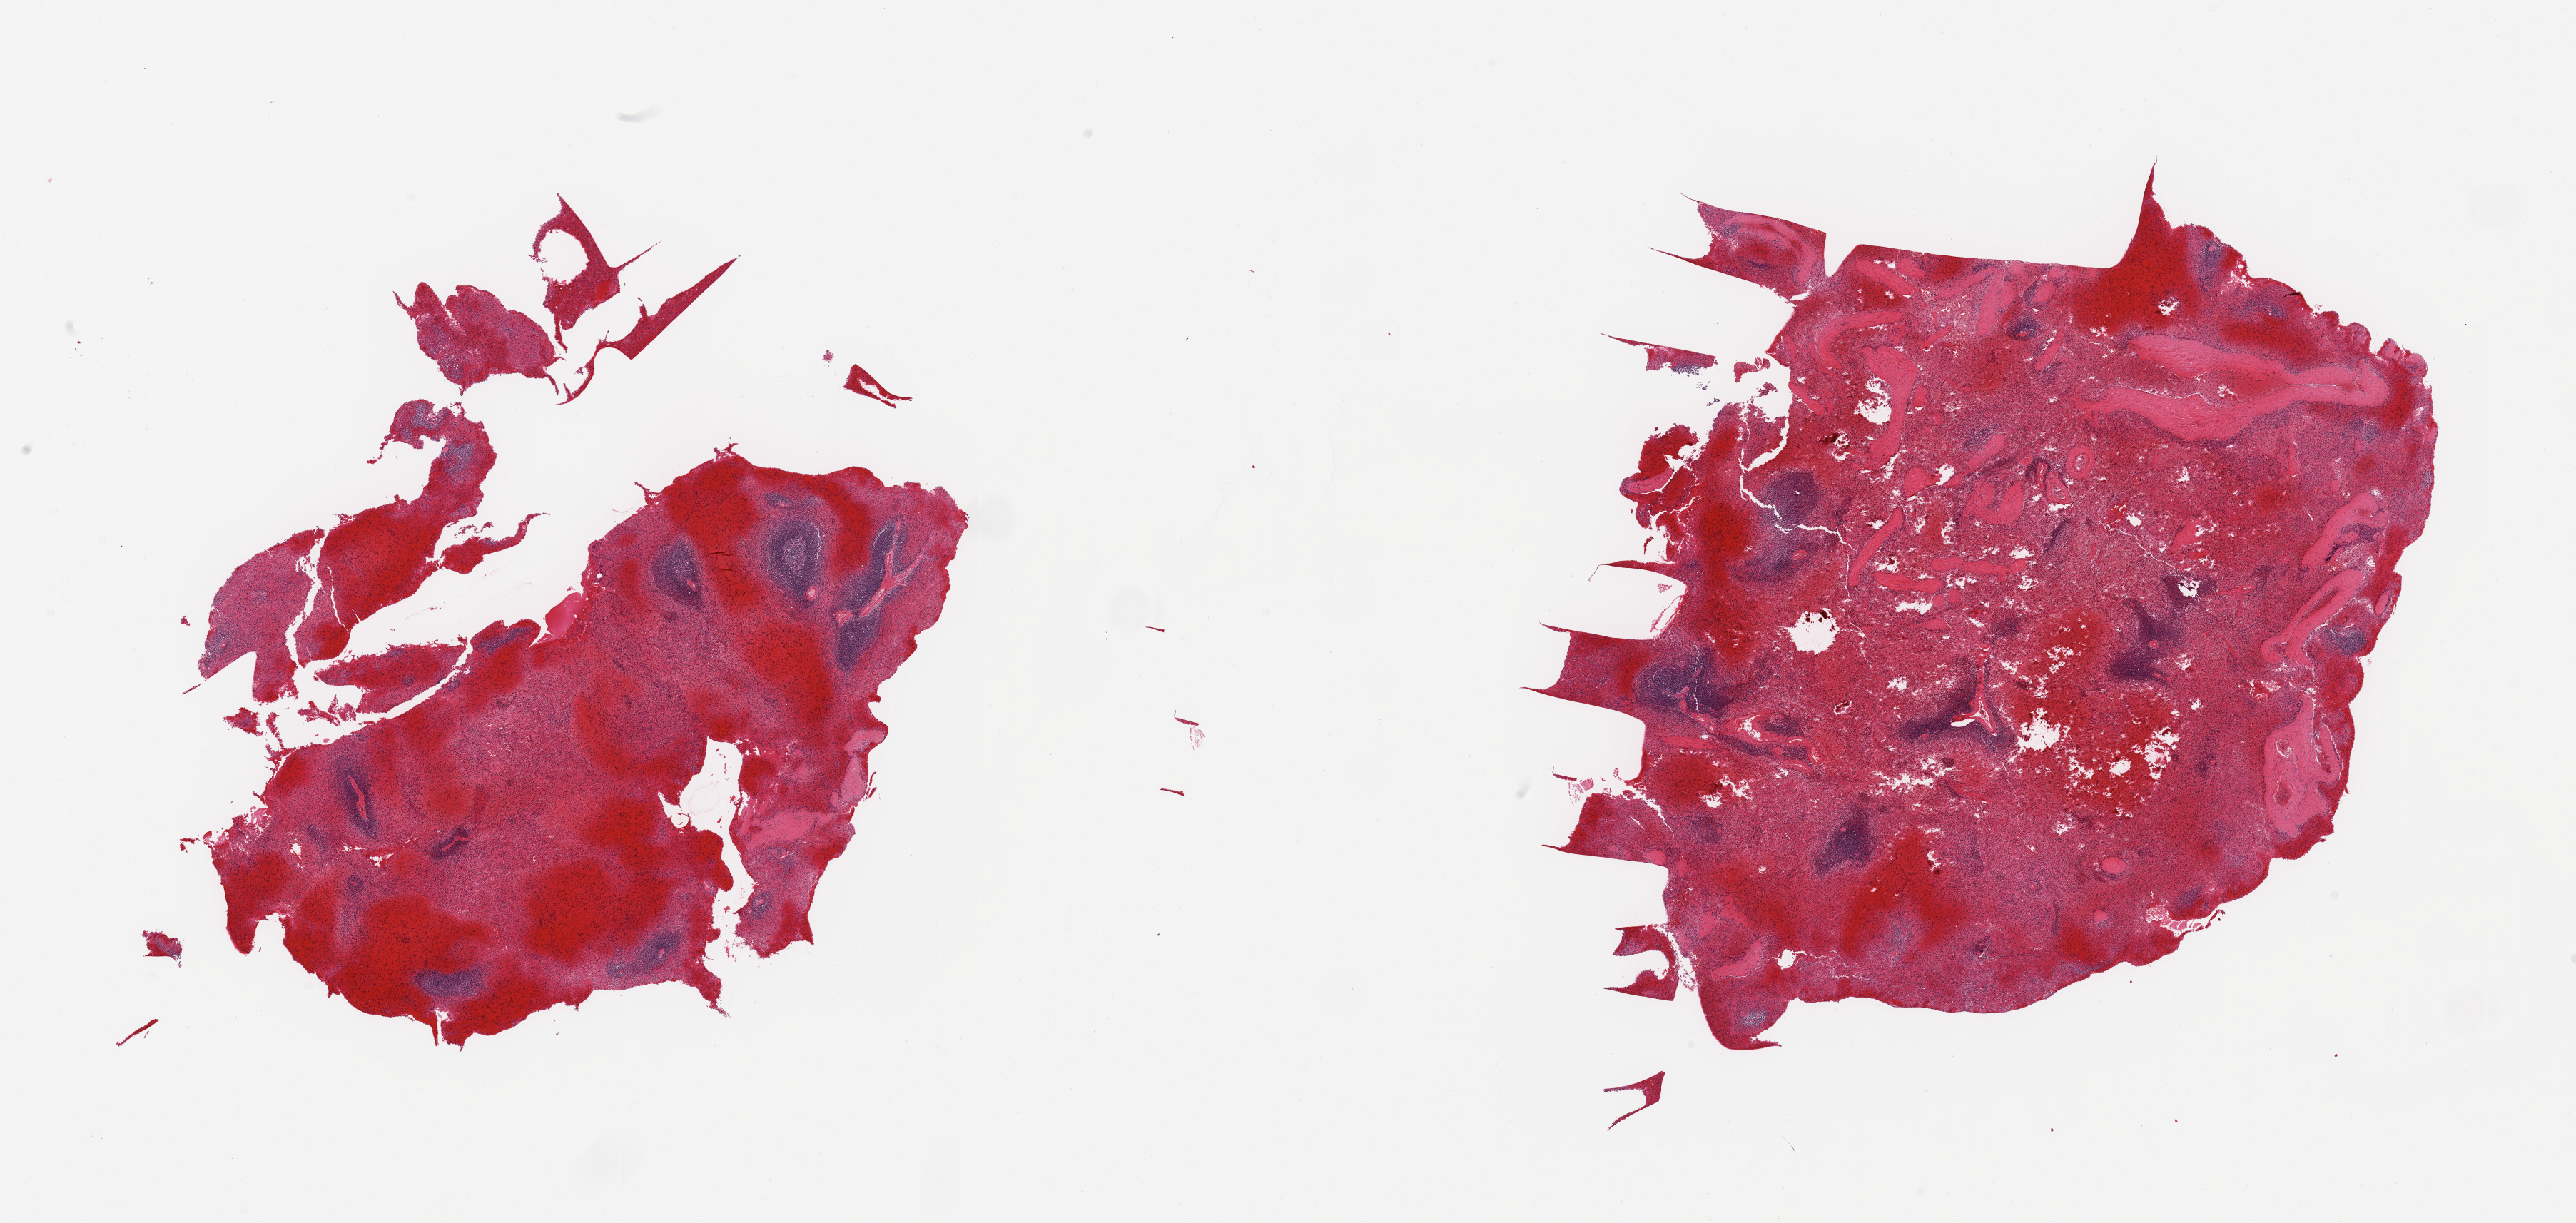
Whole-slide image, H&E stain — whole scanned area (about 28.5 x 13.6 mm, from a 20x scan) shown as a low-resolution overview. PAXgene-fixed paraffin-embedded (PFPE) section. Target tissue: spleen. Tissue donor sample. Male donor.
Review note (as recorded): 2 pieces, marked congestion.